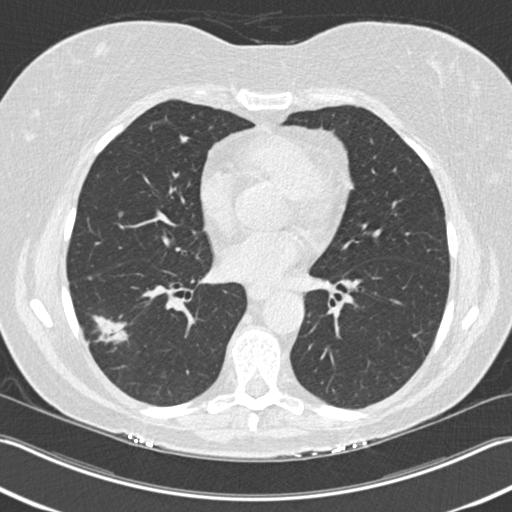
Axial slice from a low-dose chest CT screening exam, first (baseline) screen, lung window (W 1500 / L -600 HU), 2 mm slice thickness, slice 103 of 211 in the series. Female, age 63 years at enrolment. Current smoker at enrolment.
Lesion marked by an expert reader, box from (x=69, y=308) to (x=134, y=369) px. The screening reader recorded 3 non-calcified nodules or masses ≥4 mm on this exam (right upper lobe, right lower lobe, right lower lobe); which of them this box marks is not recorded. Official screen result: positive, change unspecified: nodule(s) >= 4 mm or enlarging nodule(s), mass(es), or other non-specific abnormalities suspicious for lung cancer. Participant outcome: lung cancer diagnosed 57 days after this screen — bronchiolo-alveolar adenocarcinoma, NOS, right lower lobe, well differentiated (G1), stage IA (AJCC 6th edition), 25 mm at pathology.